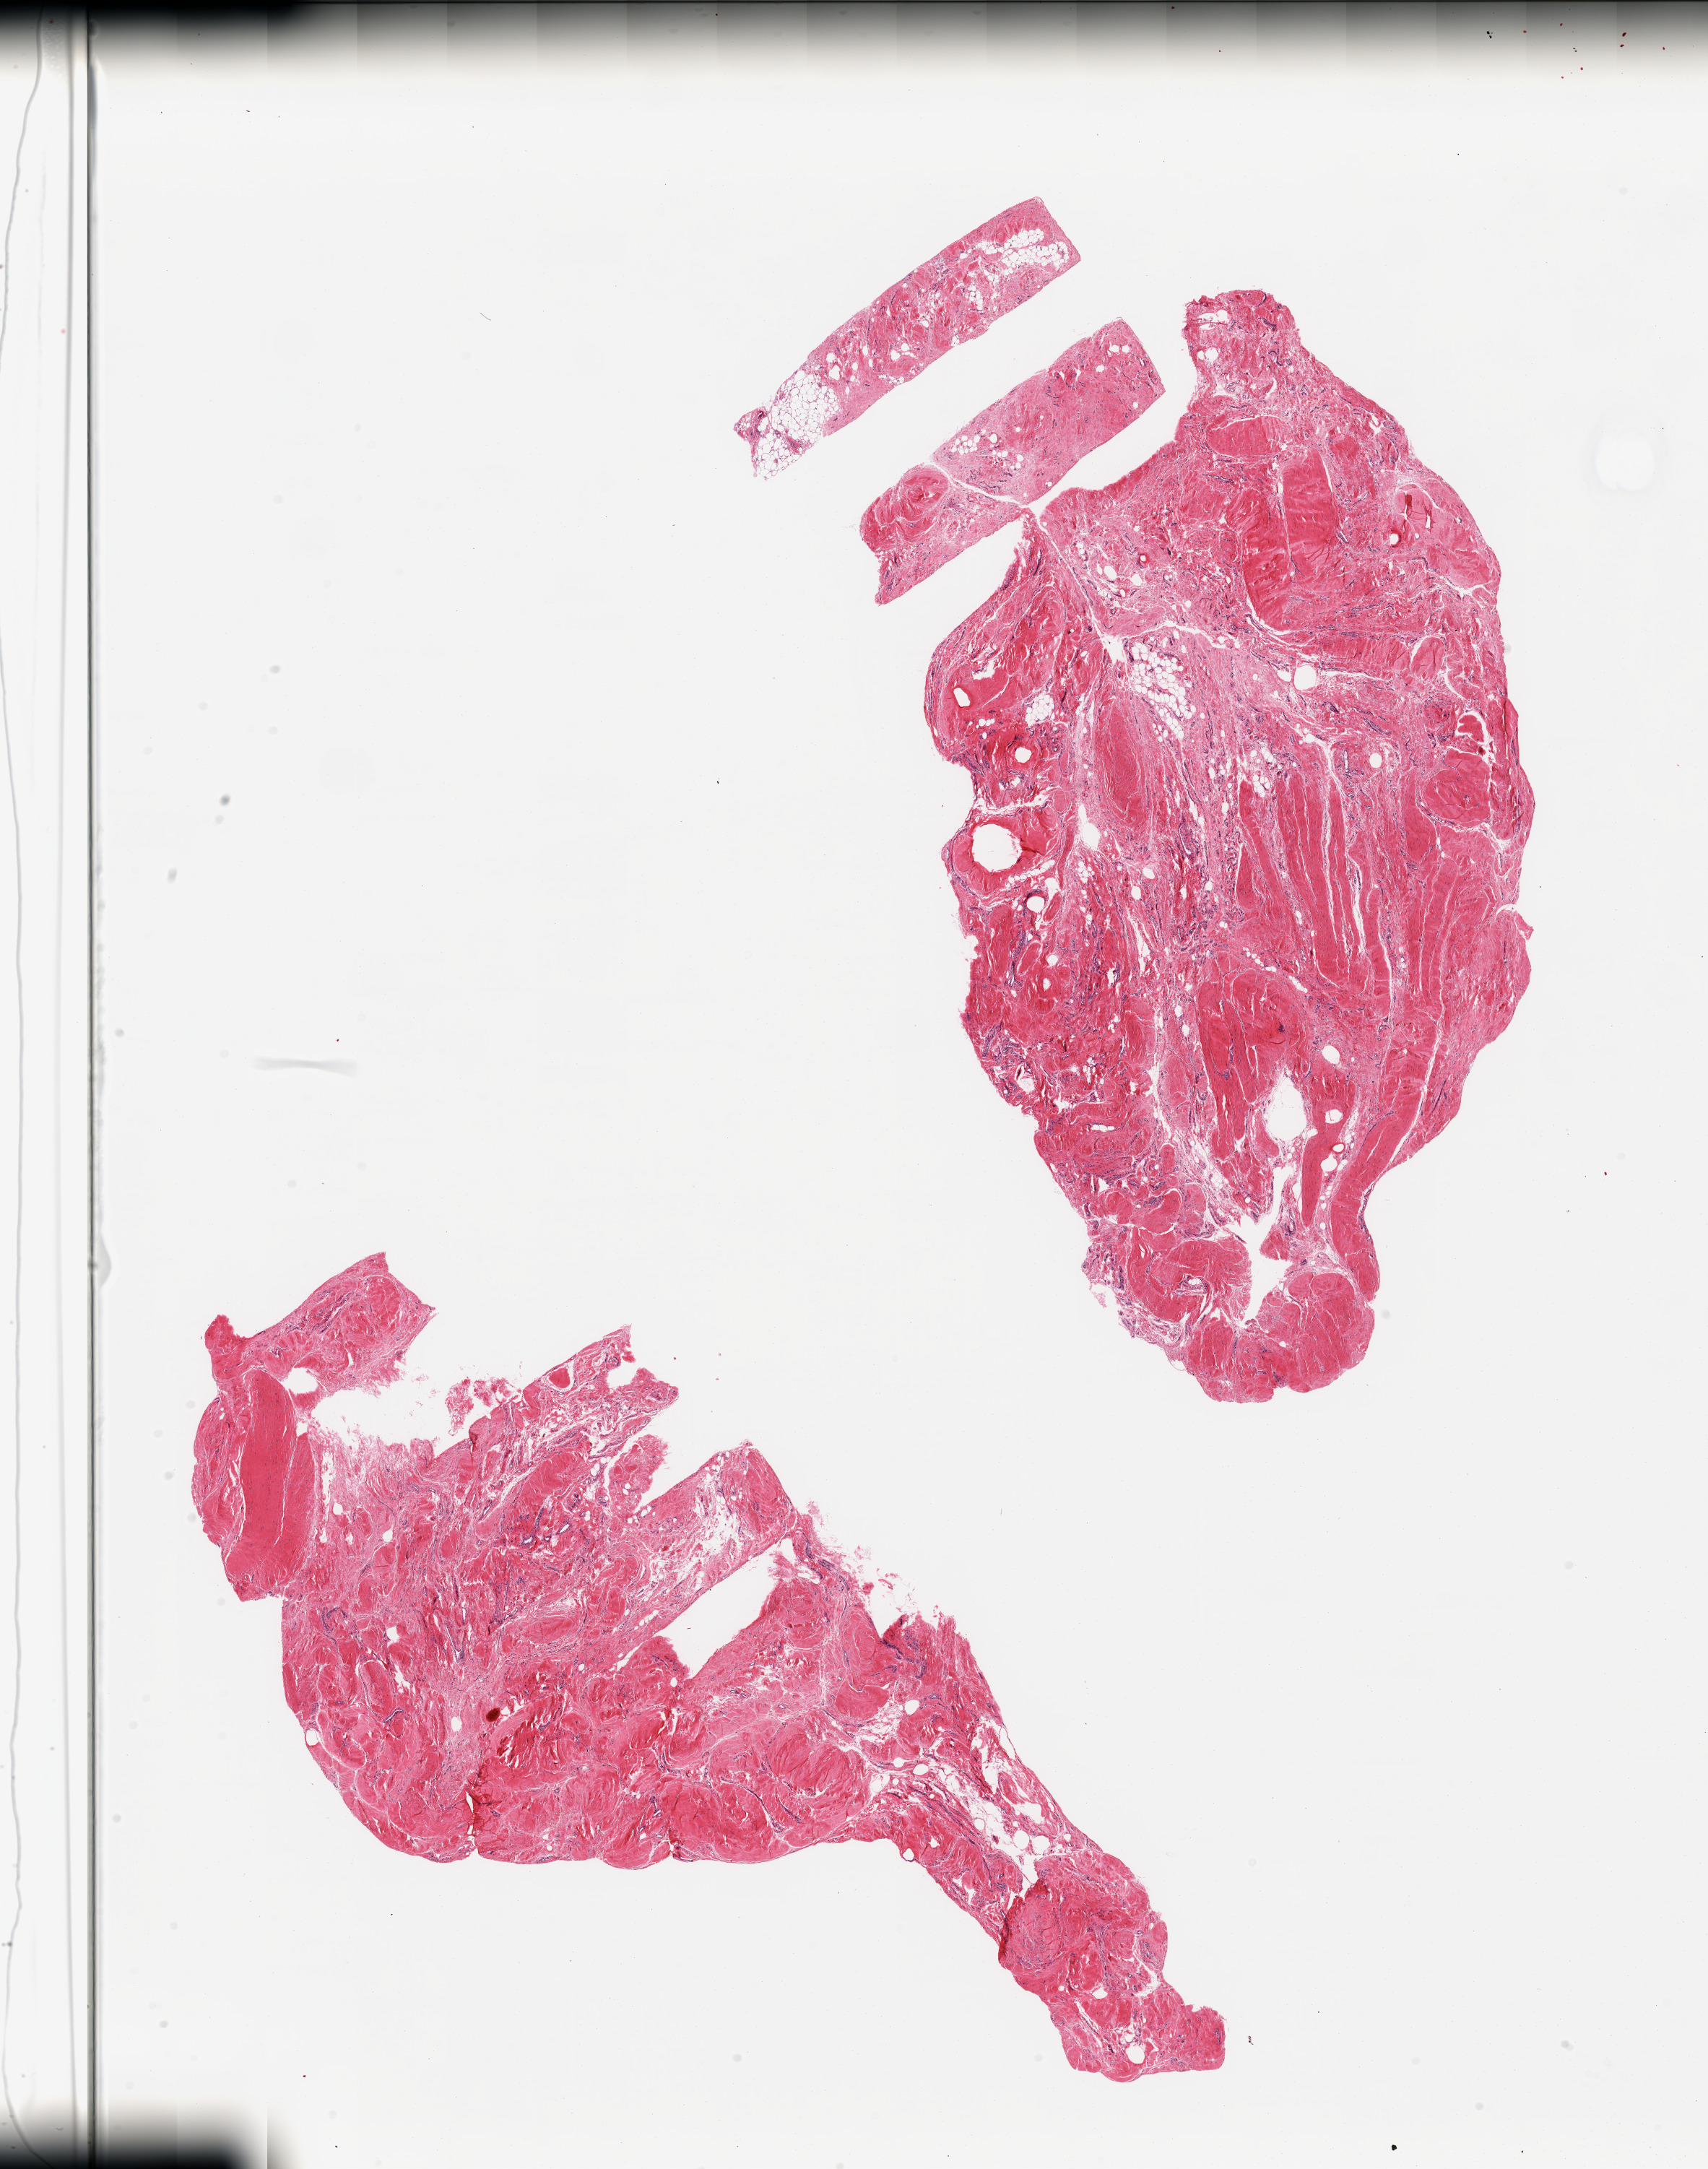
Digitized H&E-stained section — low-resolution overview of the scanned area, about 18.7 x 23.7 mm (from a 20x scan). PAXgene-fixed, paraffin-embedded tissue. Section of breast (target tissue). Donor tissue sample.
Reviewer comment on this tissue sample: 2 pieces; abundant fibrocollagenous tissue; no ductal structures present.